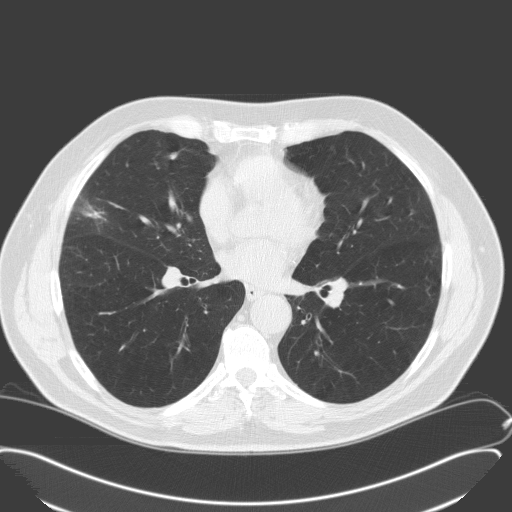
Low-dose screening chest CT, axial slice. Second annual screen. Lung window (W 1500 / L -600 HU). Standard (soft-tissue) reconstruction kernel (C). Slice 91 of 175 in the series. 512 × 512 image matrix, field of view 400 × 400 mm. Male participant, aged 65 years at enrolment. Former smoker at enrolment.
Expert-annotated lung lesion, box from (x=50, y=190) to (x=117, y=244) px. Screening reader's record for this exam: no non-calcified nodule ≥4 mm recorded. Lung cancer was diagnosed 346 days after this screen: adenocarcinoma, NOS, right middle lobe, moderately differentiated (G2), stage IA (AJCC 6th edition), 25 mm at pathology.